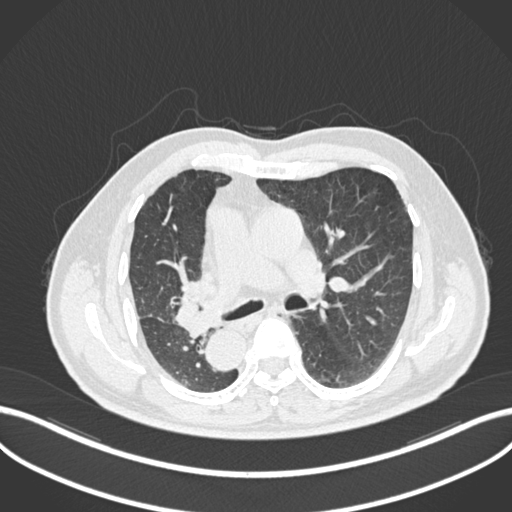
Chest CT, one axial slice; position 133 of 206 along the scan axis; lung window (W 1500 / L -600 HU); 1 mm slice thickness; 512 × 512 image matrix. Patient: male, 67 years. From the clinical record (not read from this slice): clinical TNM (as recorded): T2a N0 M0.
Structures marked on this image (bounding box drawn by a radiologist):
- lung tumour (recorded histology: squamous cell carcinoma): box from (x=166, y=286) to (x=213, y=326) px